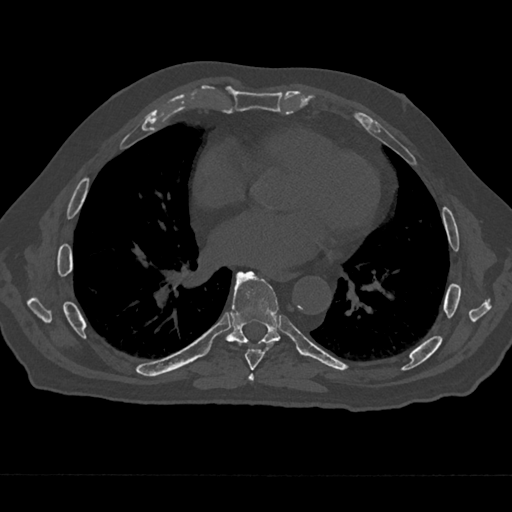
CT including the spine, one axial slice; position 342 of 797 along the scan axis; reconstruction kernel Br40s/3; 120 kVp; bone window (W 1800 / L 400 HU); 0.5 mm slice thickness; 512 × 512 image matrix, field of view 377 × 377 mm. Male patient, age 75 years. From the clinical record (not read from this slice): primary cancer: renal; vertebrae with lytic lesions (as recorded): T4.
Outlined on this slice (semi-automatic segmentation, software-assisted and operator-edited):
- T6 vertebra: bounding box (x1, y1, x2, y2) in pixels: (248, 373, 255, 382)
- T7 vertebra: (238, 272, 276, 370)
- T8 vertebra: (220, 271, 280, 345)